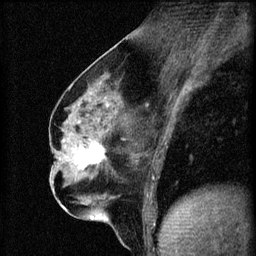
Breast MRI (dynamic contrast-enhanced), one sagittal slice. Position 31 of 60 along the scan axis. 3 images stored at this slice position (order not interpretable as contrast timing). 1.5 T. TE 4.2 ms, TR 8.2 ms. 2 mm slice thickness. 256 × 256 image matrix. Patient: female, 56 years.
Outlined on this slice (semi-automatic segmentation, software-assisted and operator-edited):
- analysis volume of interest (the breast-tissue region the enhancement analysis was run in; not a lesion): bounding box [x1, y1, x2, y2] px = [62, 136, 111, 179]
- tumour enhancement mask (voxels above the 70 % enhancement threshold inside the analysis volume of interest): [62, 142, 104, 169]